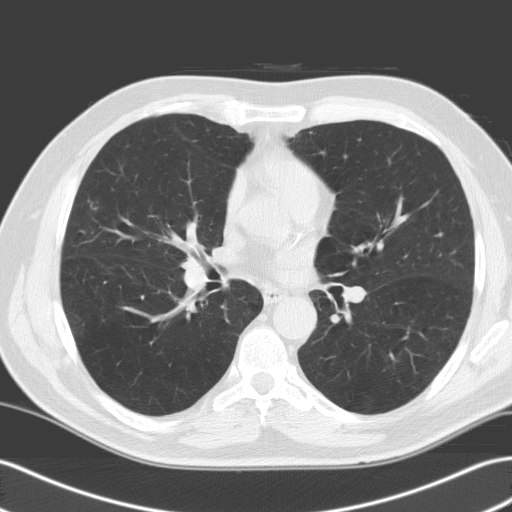
Axial slice from a low-dose chest CT screening exam, baseline screening round, lung window (W 1500 / L -600 HU), 3.2 mm slice thickness, standard (soft-tissue) reconstruction kernel (C), slice 75 of 160 in the series, 512 × 512 image matrix. Male, age 65 years at enrolment.
- Expert reader's lesion annotation, bounding box [x1, y1, x2, y2] px = [74, 188, 117, 228].
- No non-calcified nodule or mass ≥4 mm was recorded by the screening reader at this exam.
- Later outcome: lung cancer diagnosed 728 days after this screen (after the third annual screen) — adenocarcinoma, NOS, right middle lobe, moderately differentiated (G2), stage IA (AJCC 6th edition), 25 mm at pathology.